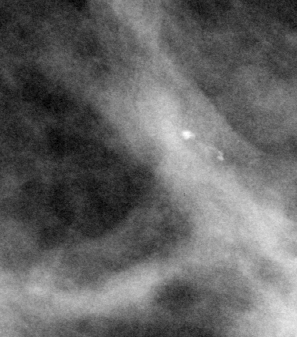
Cropped region of a digitized screen-film mammogram centred on a radiologist-marked abnormality, left breast, MLO view.
Finding: calcifications, morphology punctate, distribution clustered; BI-RADS assessment category 4; pathology (as recorded): benign.